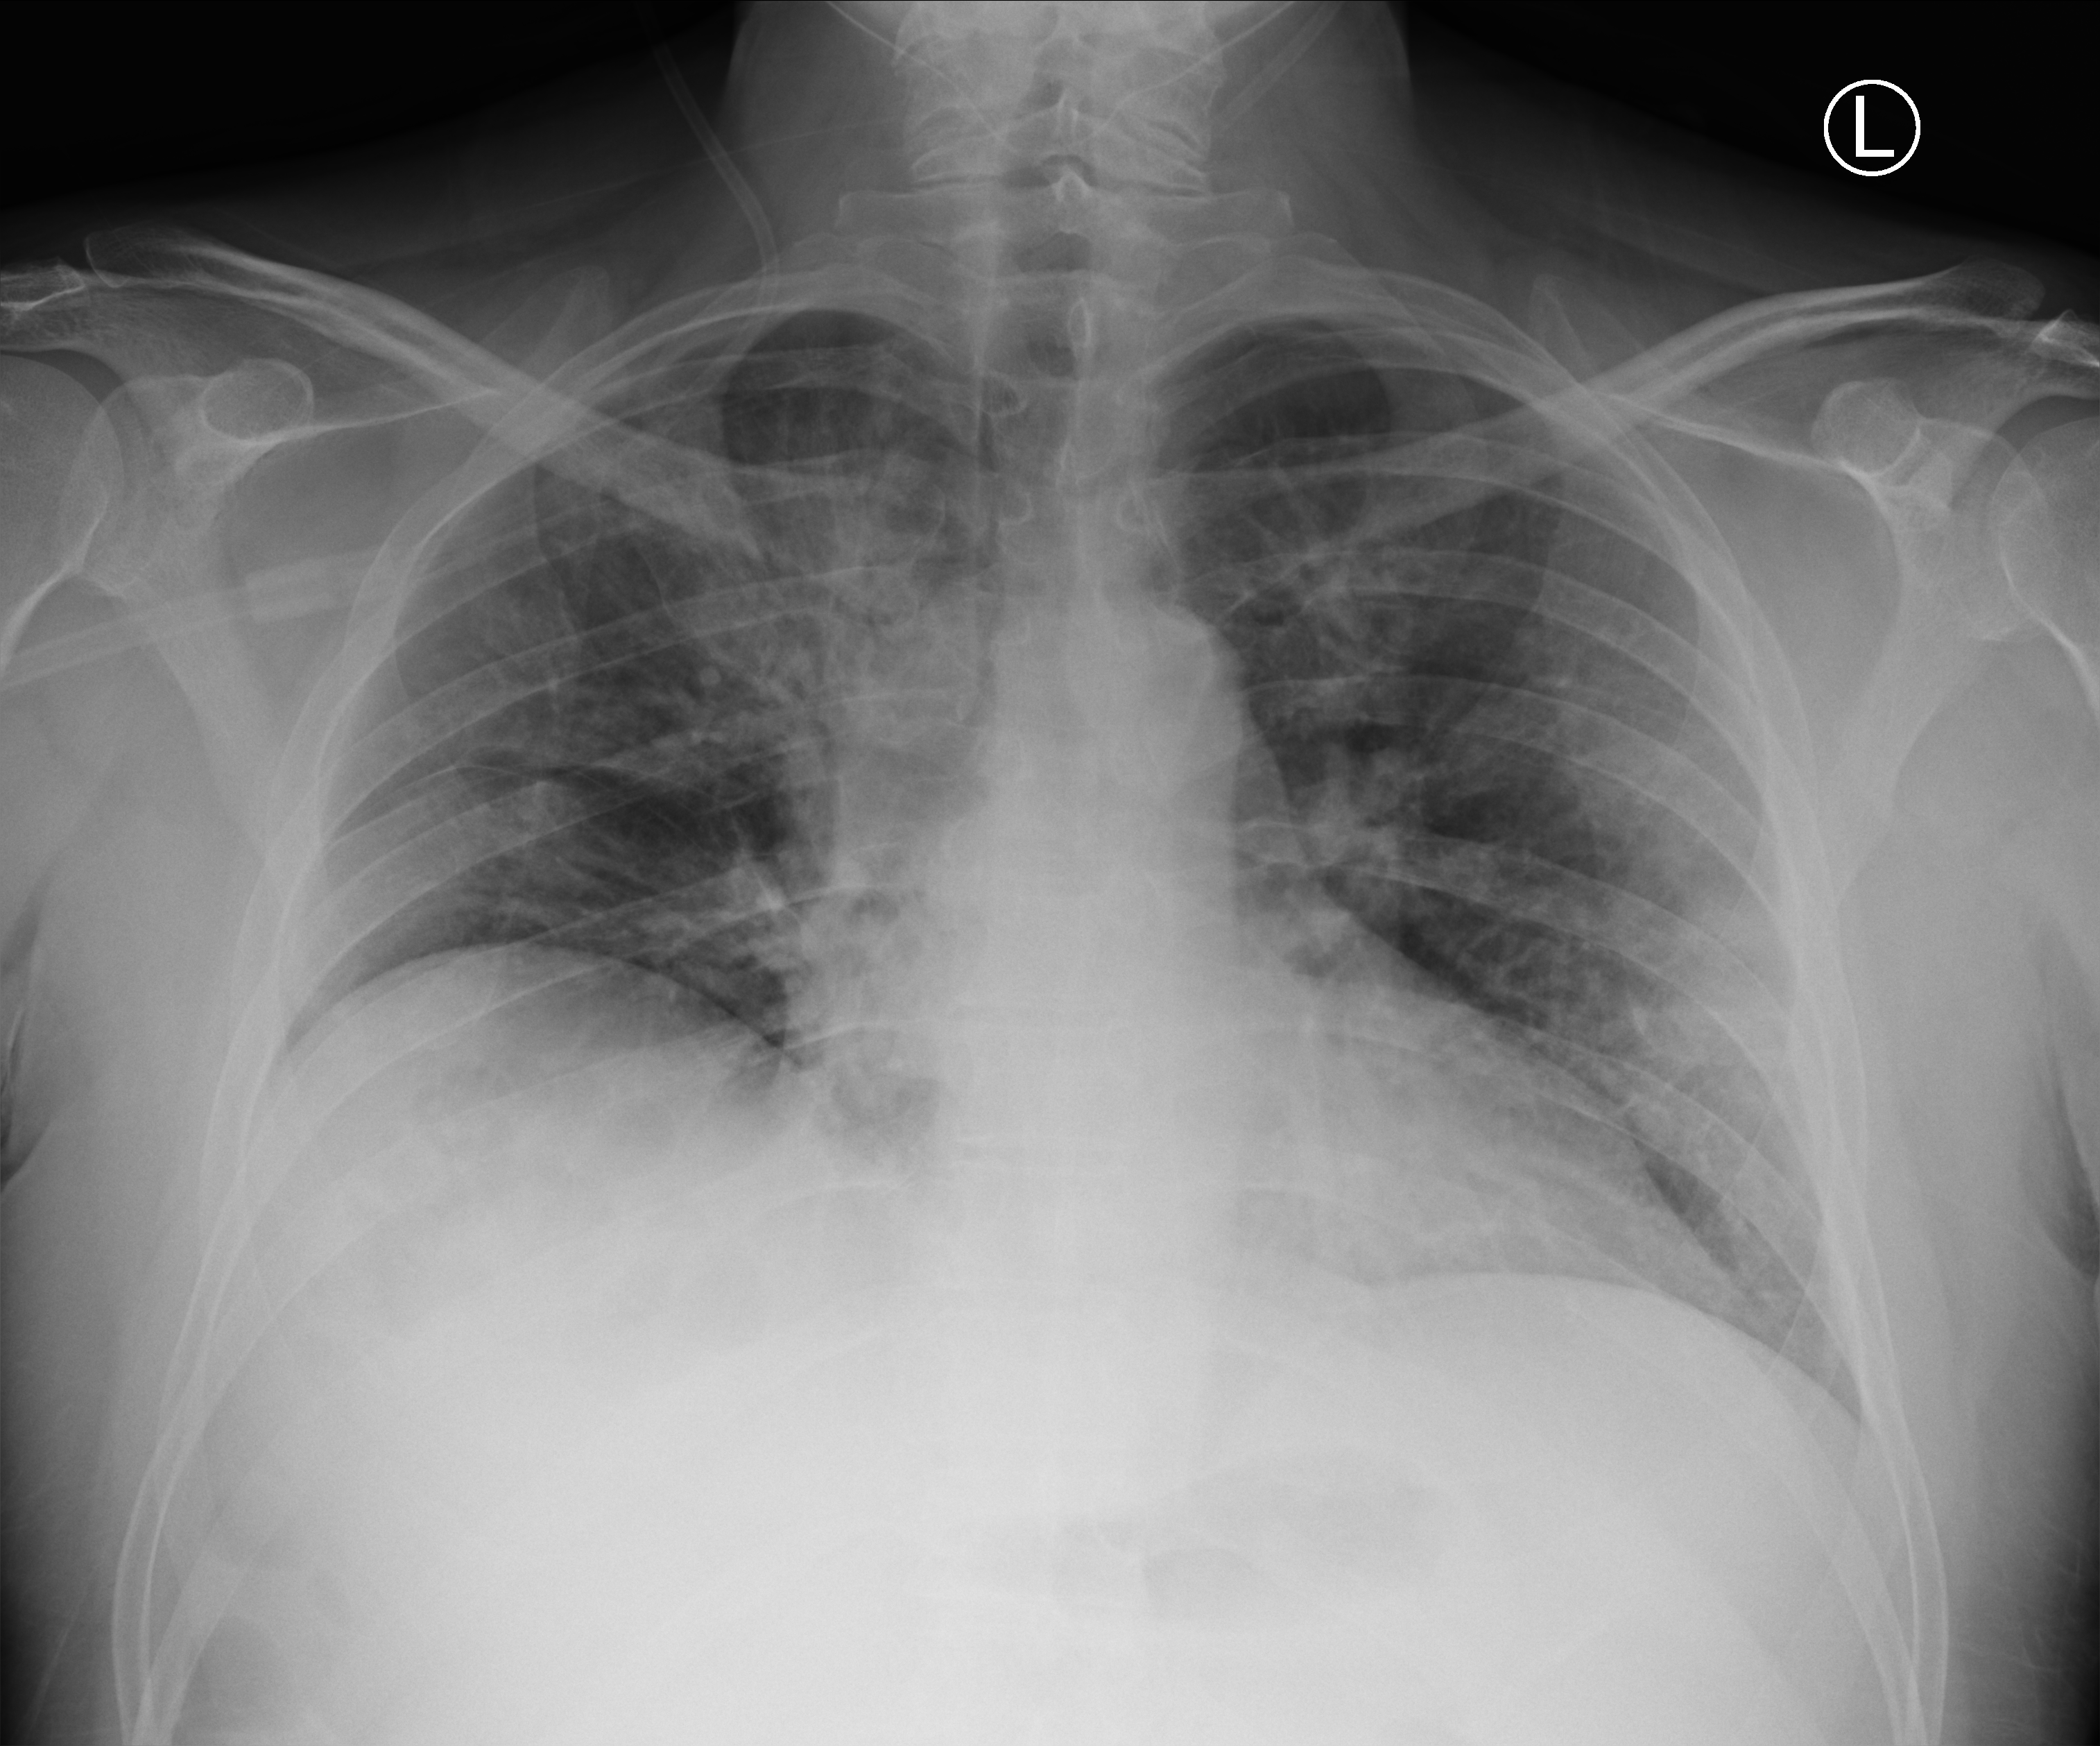
Bedside chest radiograph (computed radiography); anteroposterior (AP) projection. Male patient hospitalised with COVID-19, age 18–59 years.
From the hospital-stay record, not from the radiograph (when in the stay this image was taken is not recorded): mechanically ventilated during this hospital stay: yes; chronic kidney disease (admission record): no.